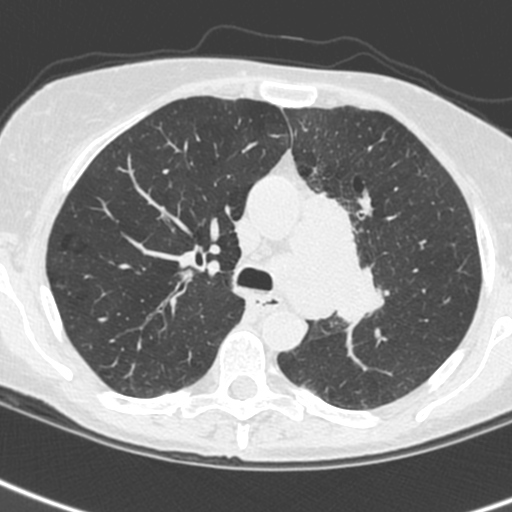
Low-dose screening chest CT, one axial slice. Slice 166 of 242 in the series (ordered by position). 120 kVp. Lung window (W 1500 / L -600 HU). 1.3 mm slice thickness. 512 × 512 image matrix.
Annotated regions visible in this slice (outlined manually by an expert reader):
- lesion 3 (tumor, upper lobe of left lung): bounding box (x1, y1, x2, y2) in pixels: (309, 192, 386, 326)